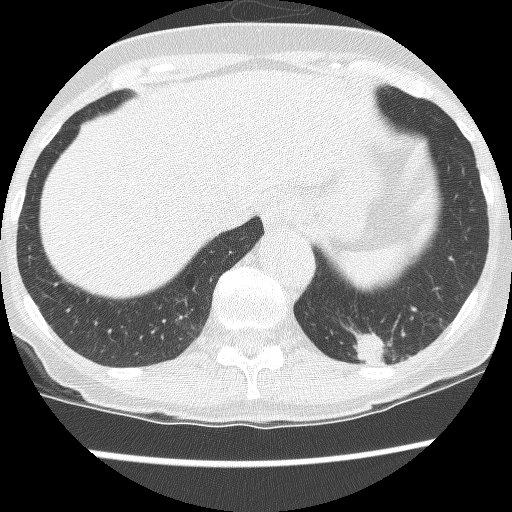
Chest CT (low-dose screening protocol), one axial image. Third screening round (two years after baseline). Lung window (W 1500 / L -600 HU). 2.5 mm slice thickness. 120 kVp. Female participant, aged 61 years at enrolment.
- Expert-annotated lung lesion, bounding box (x1, y1, x2, y2) in pixels: (336, 295, 440, 385).
- The screening reader recorded 2 non-calcified nodules or masses ≥4 mm on this exam (left lower lobe, left lower lobe); which of them this box marks is not recorded.
- Official screen result: positive, no significant change: stable abnormalities potentially related to lung cancer, unchanged since the prior screening exam.
- Participant outcome: lung cancer diagnosed 166 days after this screen — non-small cell carcinoma, left lower lobe, poorly differentiated (G3), stage IB (AJCC 6th edition), 100 mm at pathology.